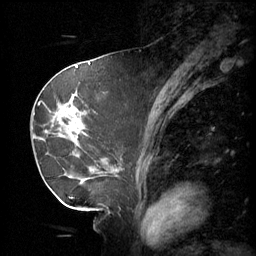
Breast MRI (dynamic contrast-enhanced), one sagittal slice. Slice 26 of 60 in the series (ordered by position). 3 images stored at this slice position (order not interpretable as contrast timing). 1.5 T. TE 4.2 ms, TR 11 ms. 2 mm slice thickness. 256 × 256 image matrix, field of view 220 × 220 mm. Female patient, age 69 years.
Outlined on this slice (semi-automatic segmentation, software-assisted and operator-edited):
- analysis volume of interest (the breast-tissue region the enhancement analysis was run in; not a lesion): bounding box [x1, y1, x2, y2] px = [36, 88, 116, 189]
- tumour enhancement mask (voxels above the 70 % enhancement threshold inside the analysis volume of interest): [58, 104, 113, 183]